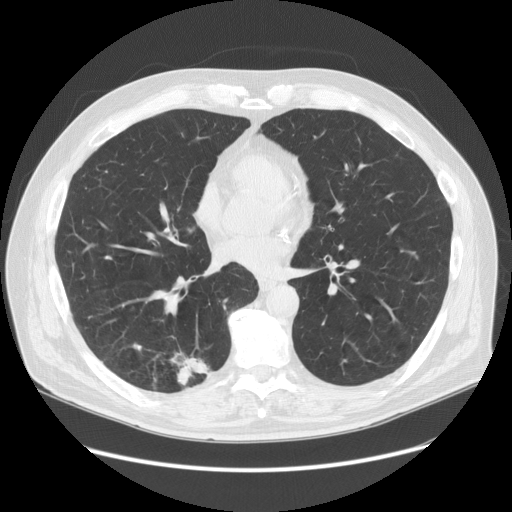
Chest CT (low-dose screening protocol), one axial image, baseline annual screen, lung window (W 1500 / L -600 HU), 2.5 mm slice thickness, standard (soft-tissue) reconstruction kernel (STANDARD), slice 83 of 149 in the series, 512 × 512 image matrix. Male, age 68 years at enrolment. Former smoker at enrolment.
Expert reader's lesion annotation, bounding box <123,332,226,406> (left, top, right, bottom; pixels). The exam's reader record, not a measurement of the box and not confirmed to be the same lesion: non-calcified nodule or mass ≥4 mm, right lower lobe, 37 × 20 mm, spiculated (stellate) margins, soft tissue attenuation. Participant outcome: lung cancer diagnosed 24 days after this screen — adenosquamous carcinoma, right lower lobe, poorly differentiated (G3), stage IIIA (AJCC 6th edition), 30 mm at pathology.